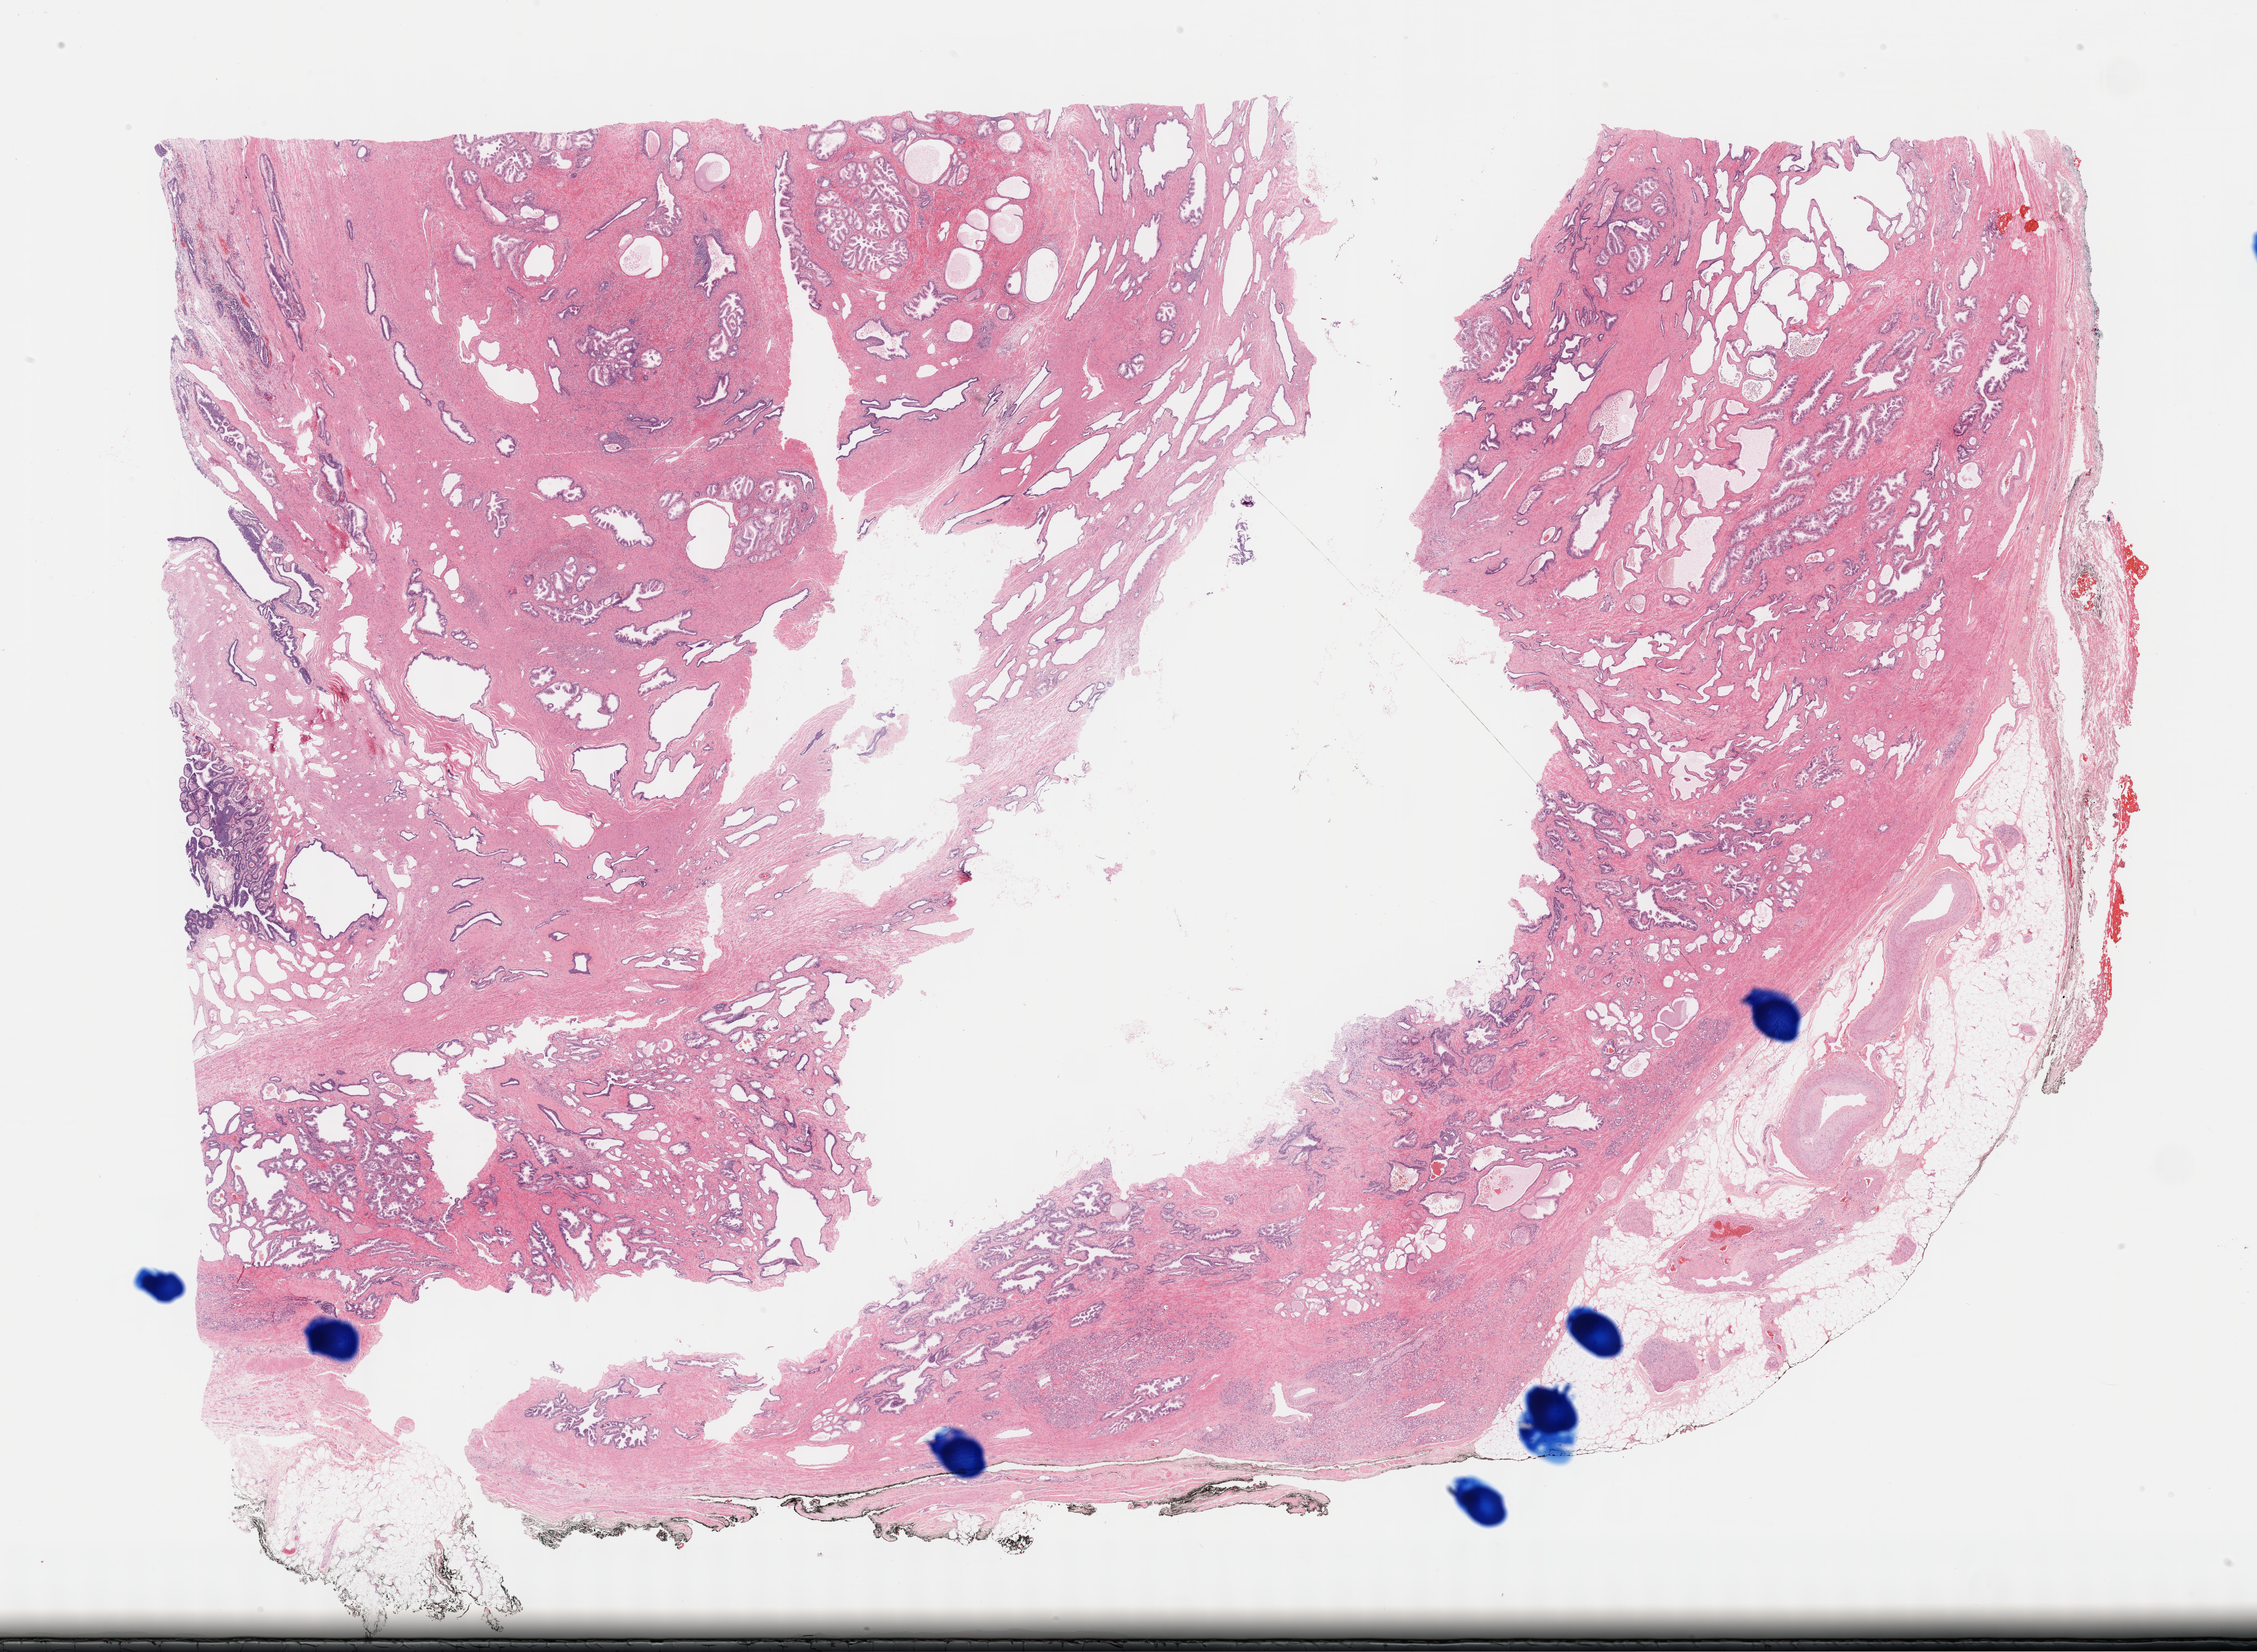
H&E whole-slide image, shown as a low-resolution overview of the whole scanned area (about 29.2 x 21.4 mm, slide scanned at 40x), FFPE section, prostate, primary tumour sample. Patient: male, age at initial diagnosis 68 years. Gleason score: 8 (4+4).
Histologic diagnosis: Signet ring cell carcinoma (prostate gland). Lymph nodes positive (case pathology): 0 of 6 examined.